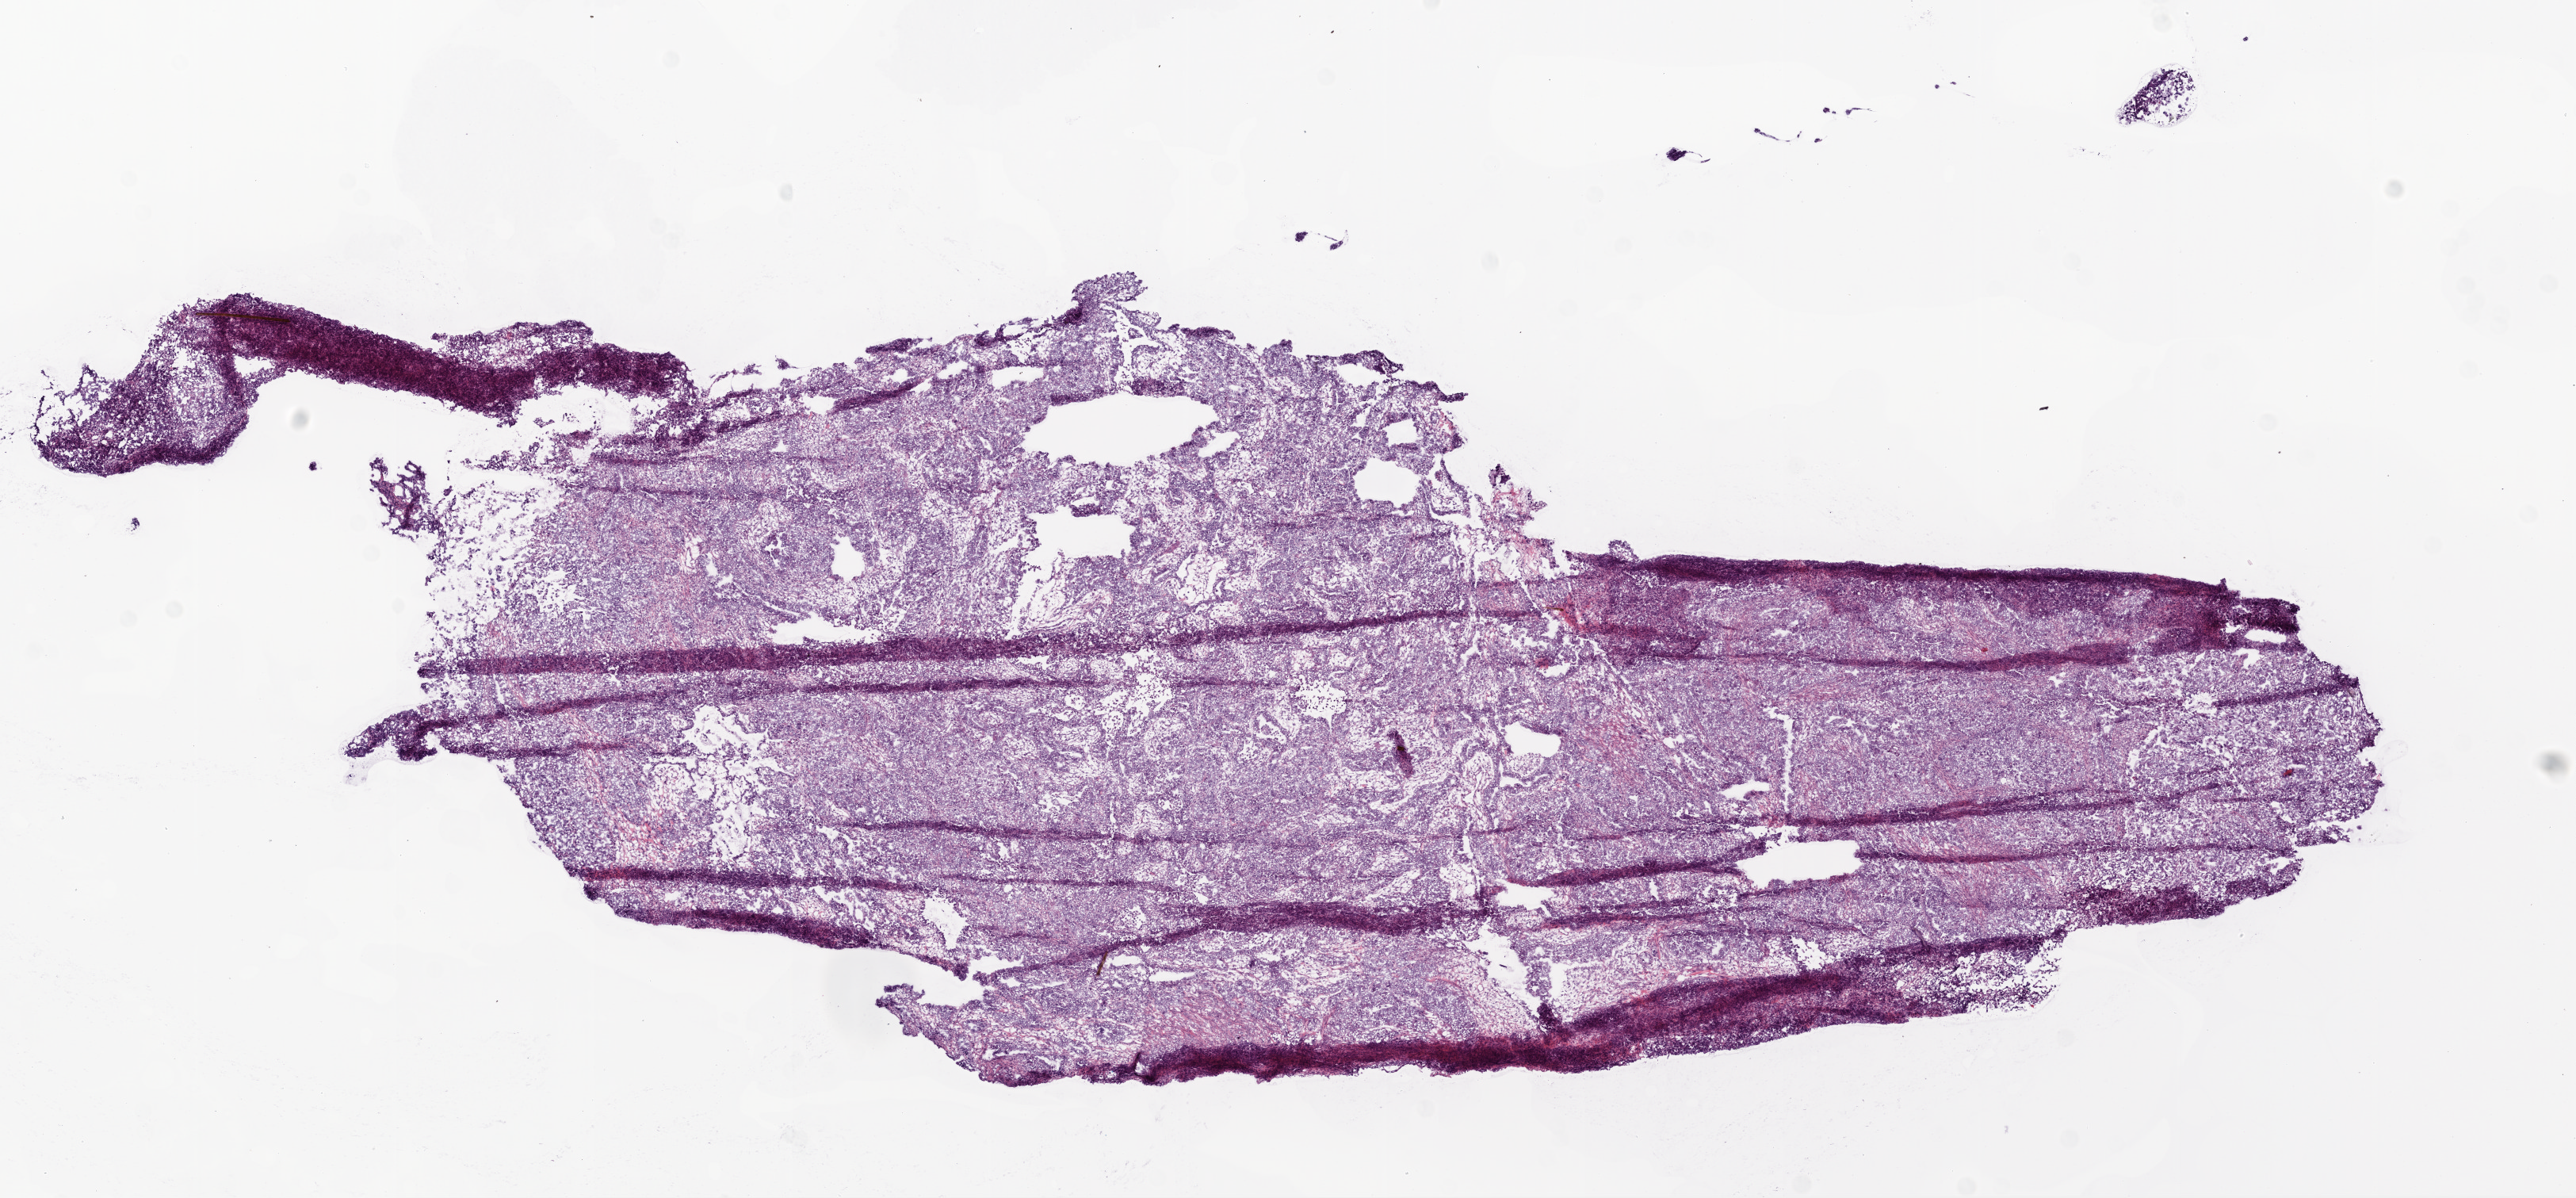
H&E-stained whole-slide image, shown as a low-resolution overview of the whole scanned area (about 13.0 x 6.1 mm); frozen section from the top of the tissue portion; sample: primary tumour, ovary. Female, age 45 years at initial diagnosis. Histologic grade: G3 (poorly differentiated). Pathologist review of this section (percent, as recorded): tumour cells 95%, tumour nuclei 95%, normal cells 0%, stromal cells 5%, necrosis 0%.
Diagnosis: Serous cystadenocarcinoma, NOS. FIGO stage: IIIC.